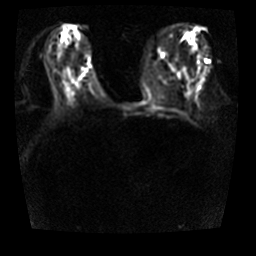
Breast MRI, one axial slice. Slice 15 of 32 in the series (ordered by position). Diffusion-weighted series; image 2 of 4 stored at this slice position (different b-values; order by instance number). 3 T. 256 × 256 image matrix, field of view 360 × 360 mm. Female patient.
Outlined on this slice (expert manual segmentation):
- tumour on diffusion-weighted imaging: box from (x=85, y=69) to (x=87, y=71) px